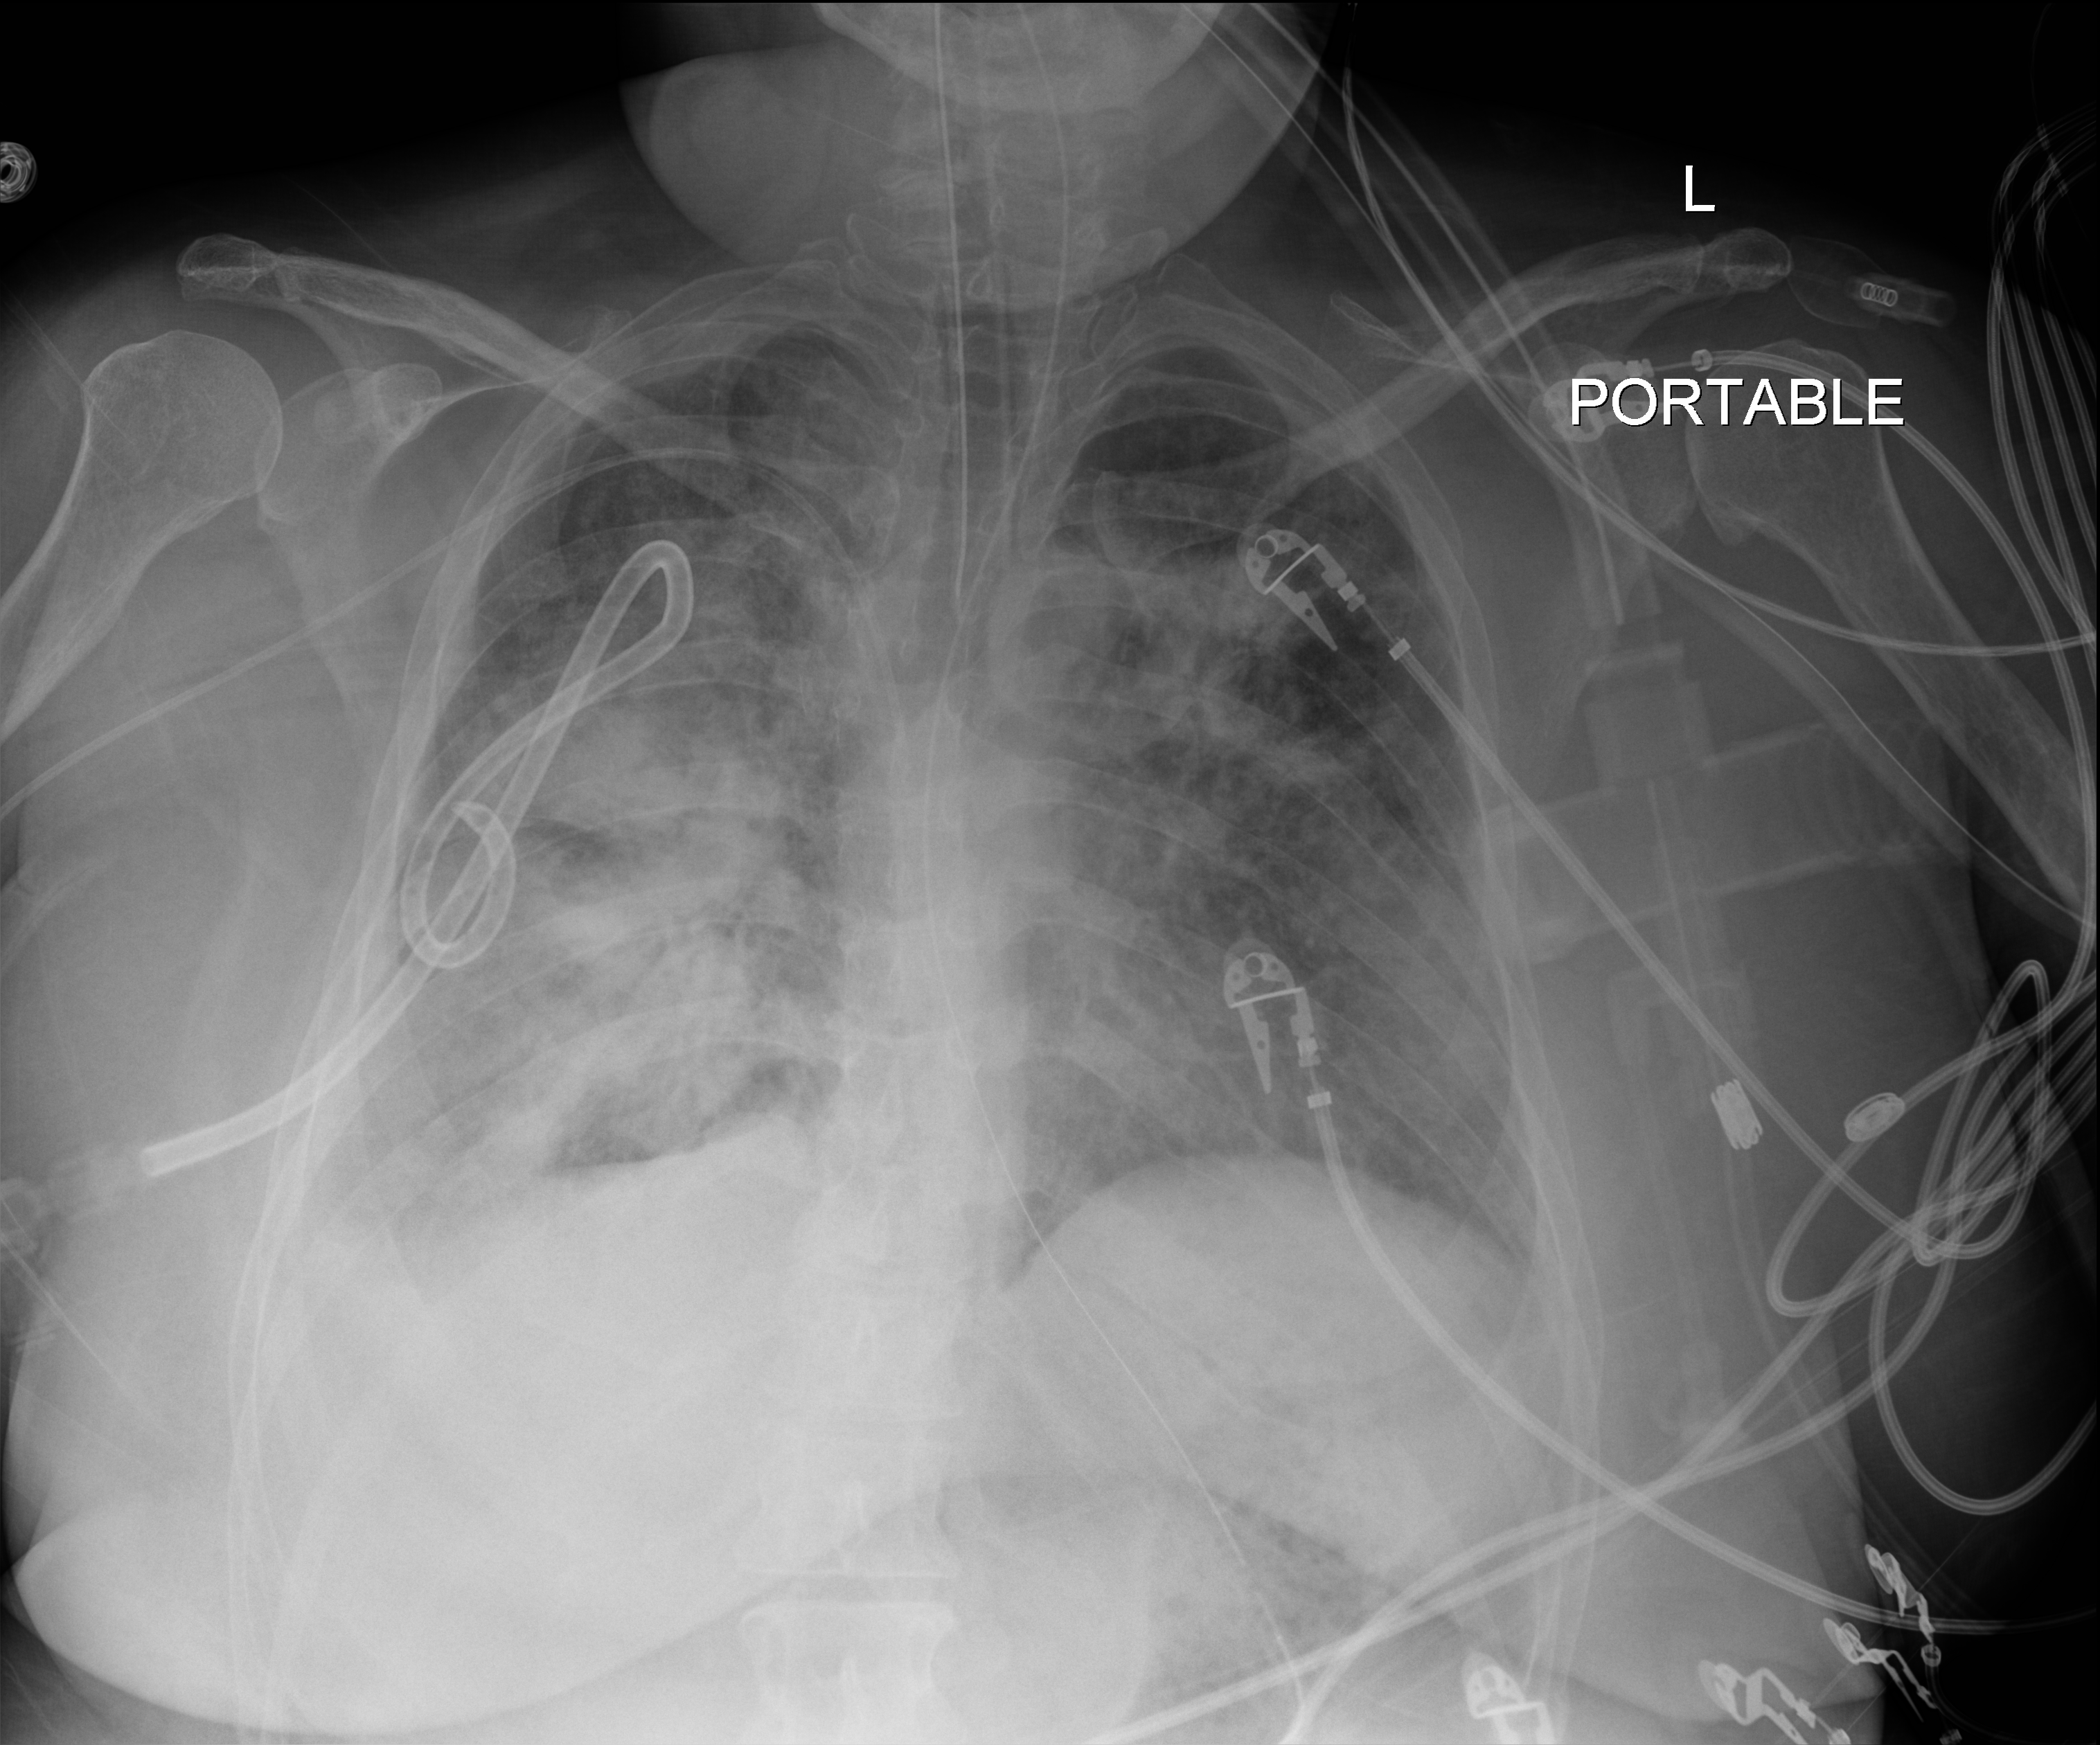
Bedside chest radiograph (digital radiography), anteroposterior (AP) projection. Adult patient hospitalised with COVID-19, age 18–59 years.
Admission-level facts for this patient (not findings on this image; timing relative to this image not recorded):
- length of hospital stay: 15 days
- admitted to intensive care during this hospital stay: yes